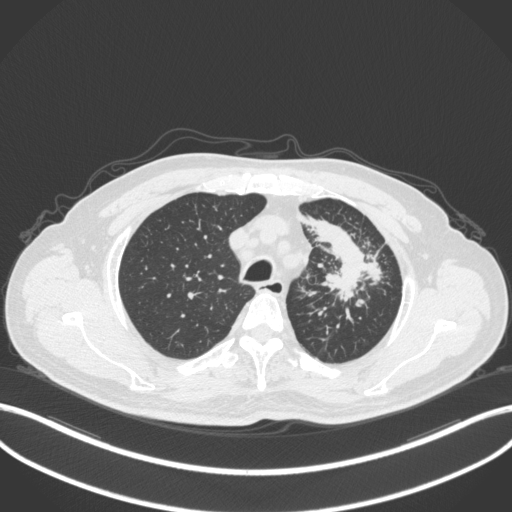
Chest CT, one axial slice. Position 282 of 386 along the scan axis. Reconstruction kernel B31f. 120 kVp. Lung window (W 1500 / L -600 HU). 1 mm slice thickness. 512 × 512 image matrix, field of view 400 × 400 mm. Male patient, age 69 years. From the clinical record (not read from this slice): clinical TNM (as recorded): T2a N2 M0; histopathological grade: G2-3.
Annotated regions visible in this slice (rectangle marked by the reading radiologist):
- lung tumour (recorded histology: adenocarcinoma): box from (x=302, y=211) to (x=388, y=307) px